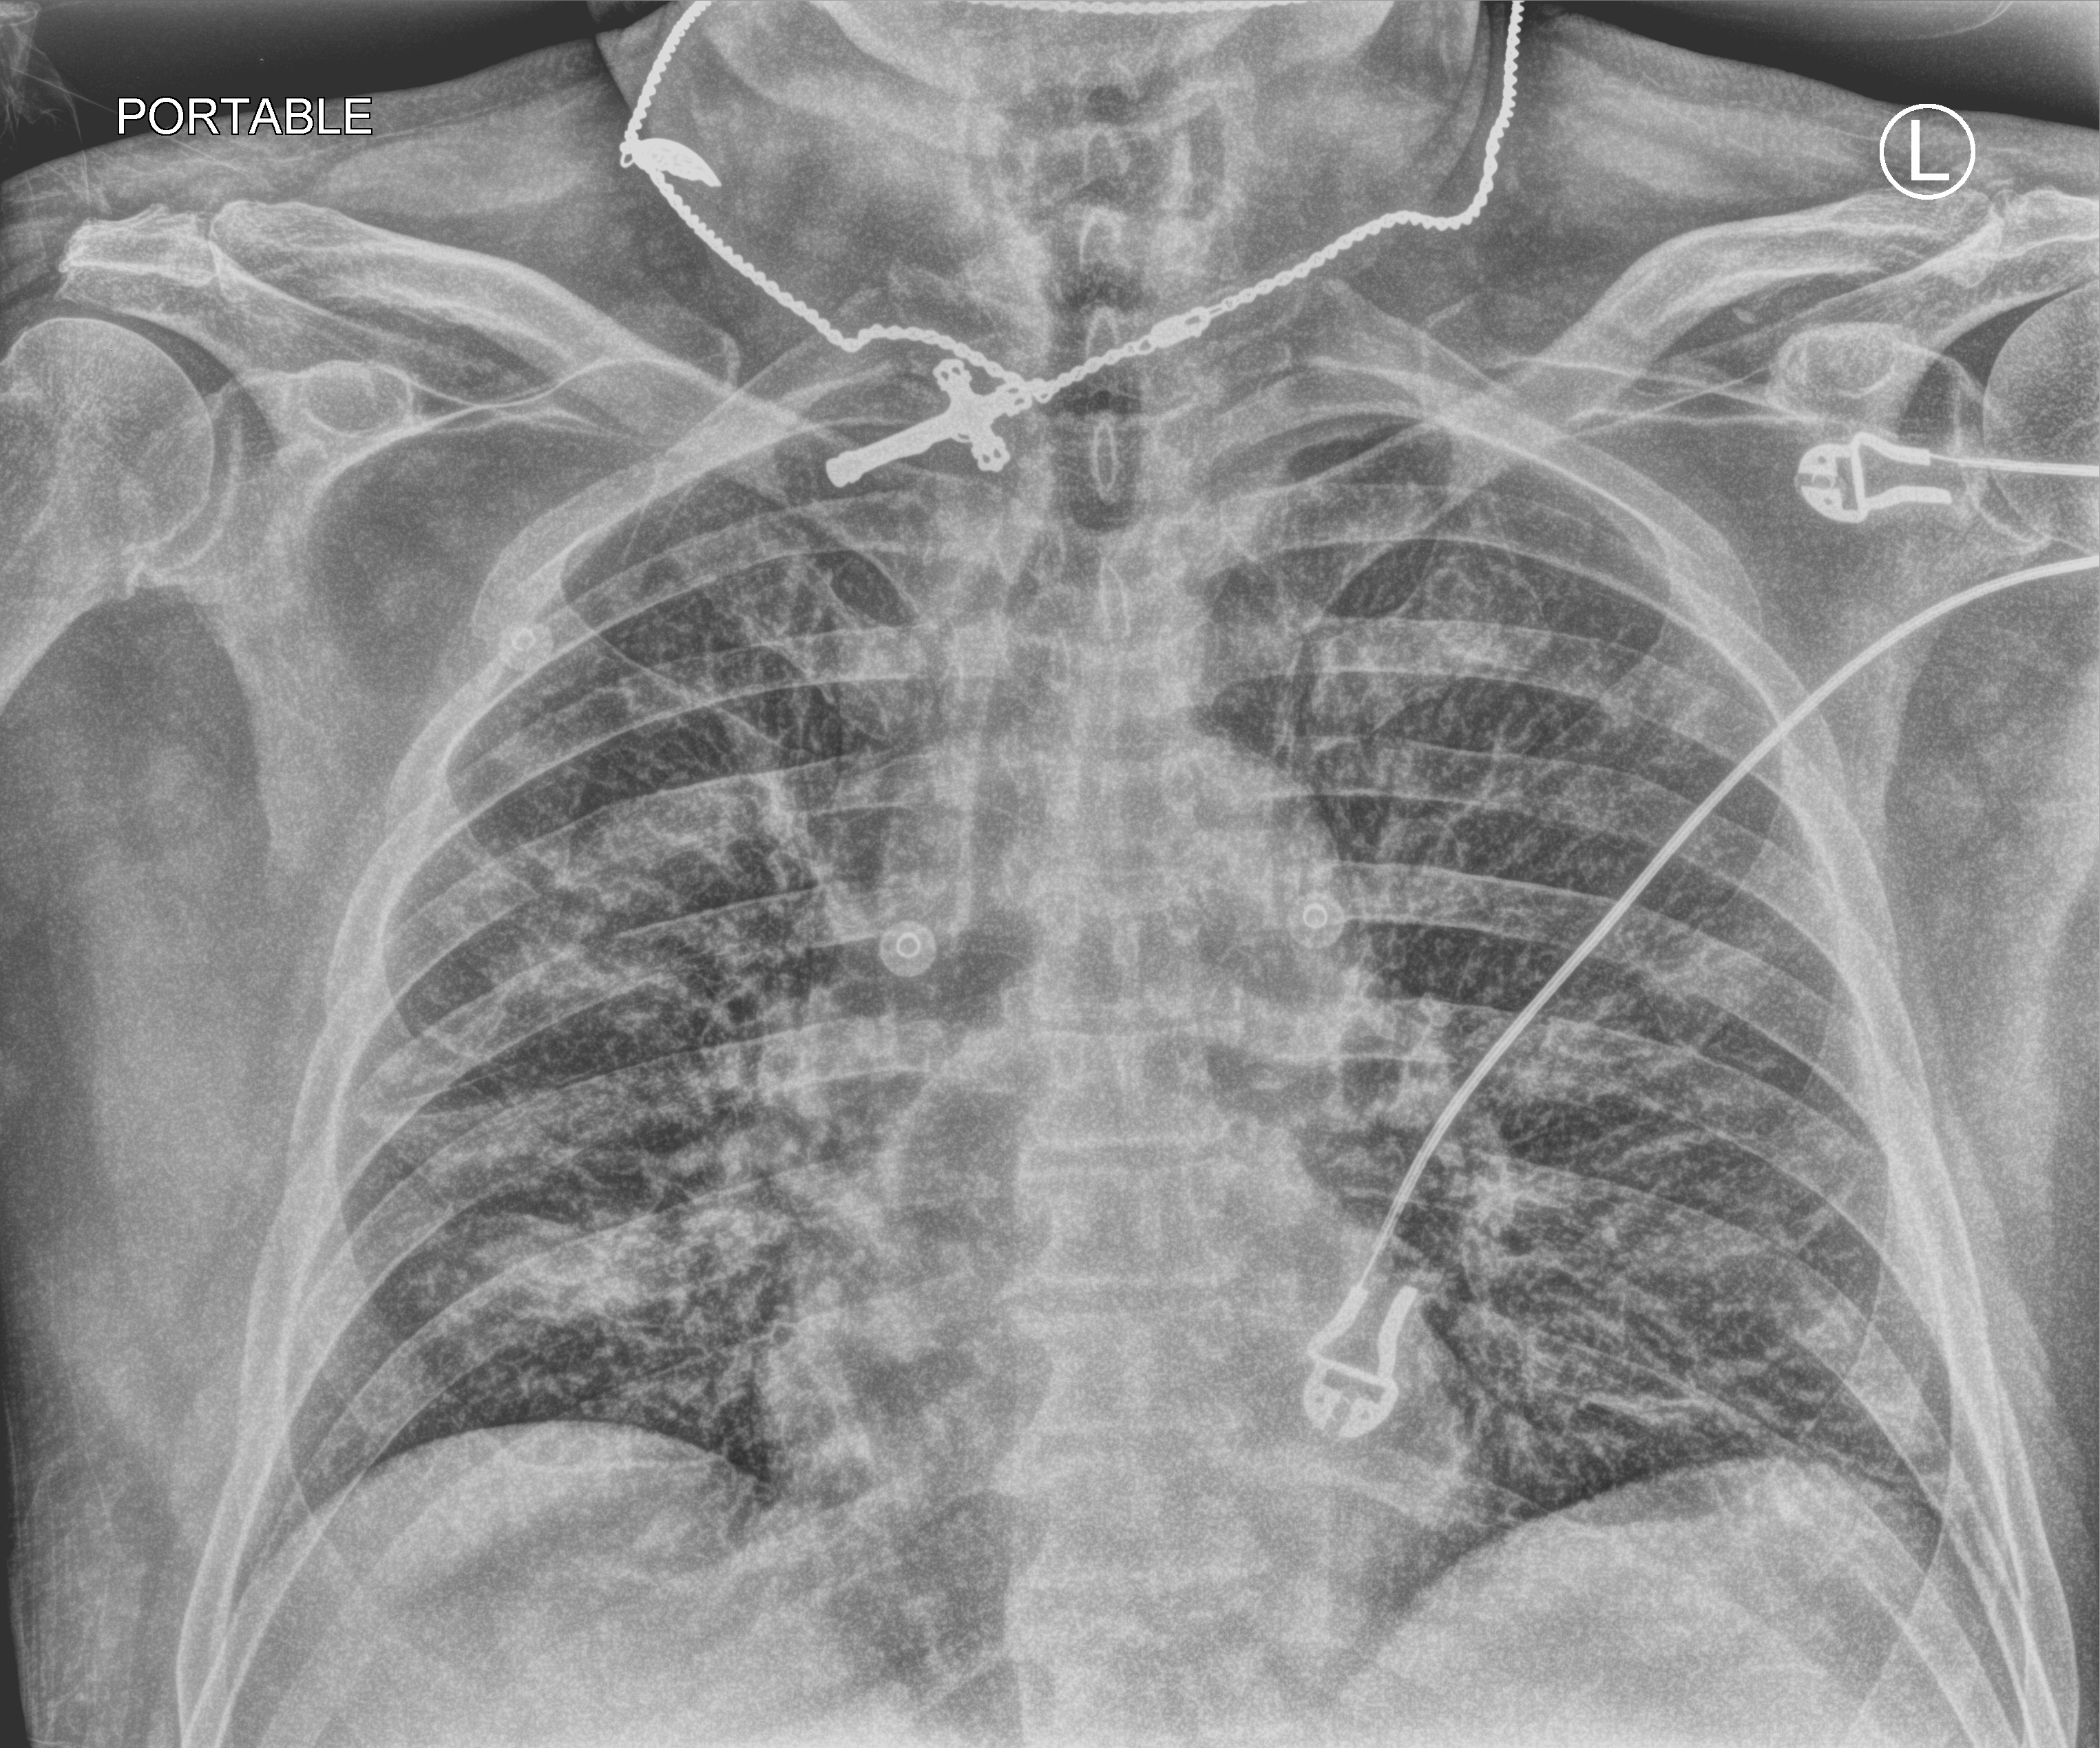
Bedside chest radiograph (computed radiography), anteroposterior (AP) projection. Male patient hospitalised with COVID-19, age 75–90 years.
Admission-level facts for this patient (not findings on this image; timing relative to this image not recorded): other chronic lung disease (admission record): no; mechanically ventilated during this hospital stay: no; admitted to intensive care during this hospital stay: no.